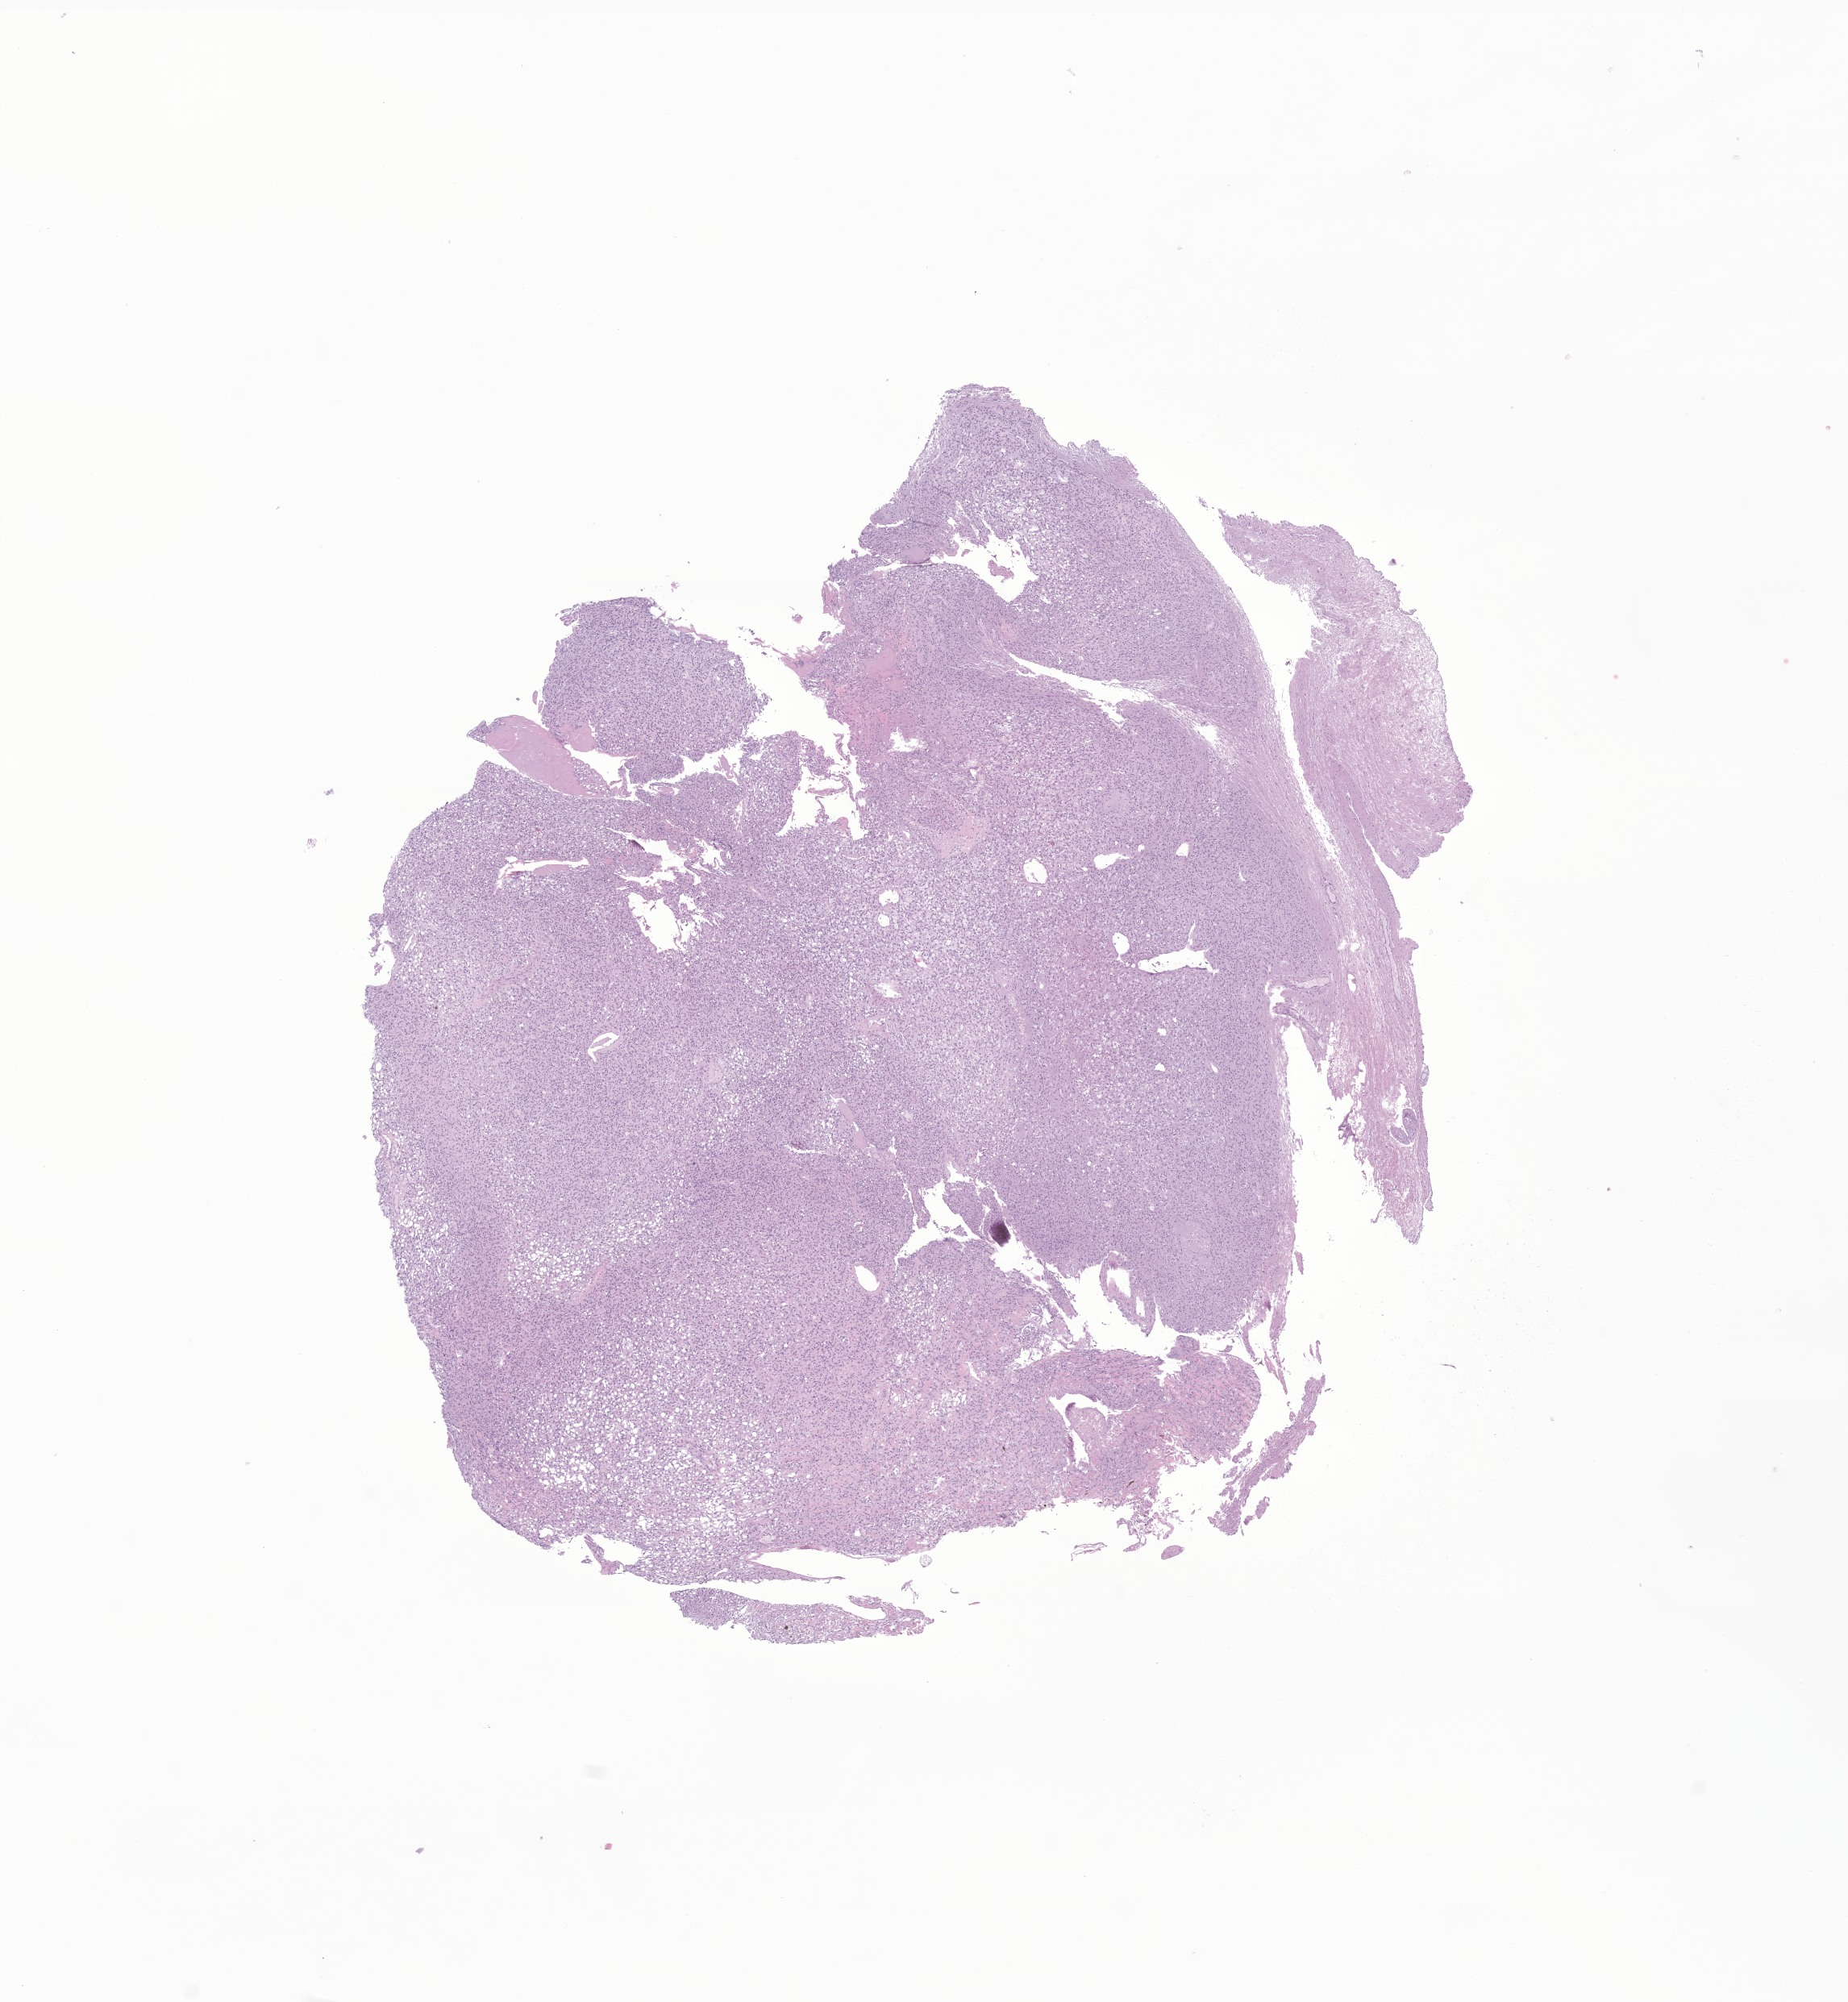
Digitized H&E-stained section of tumor tissue from the spinal cord — shown as a low-resolution overview of the whole scanned area (about 9.7 x 10.5 mm); formalin-fixed, paraffin-embedded (FFPE) tissue. Patient female; age 192 months (16 years).
Diagnosis (ICD-O-3 morphology term): Hemangioblastoma.